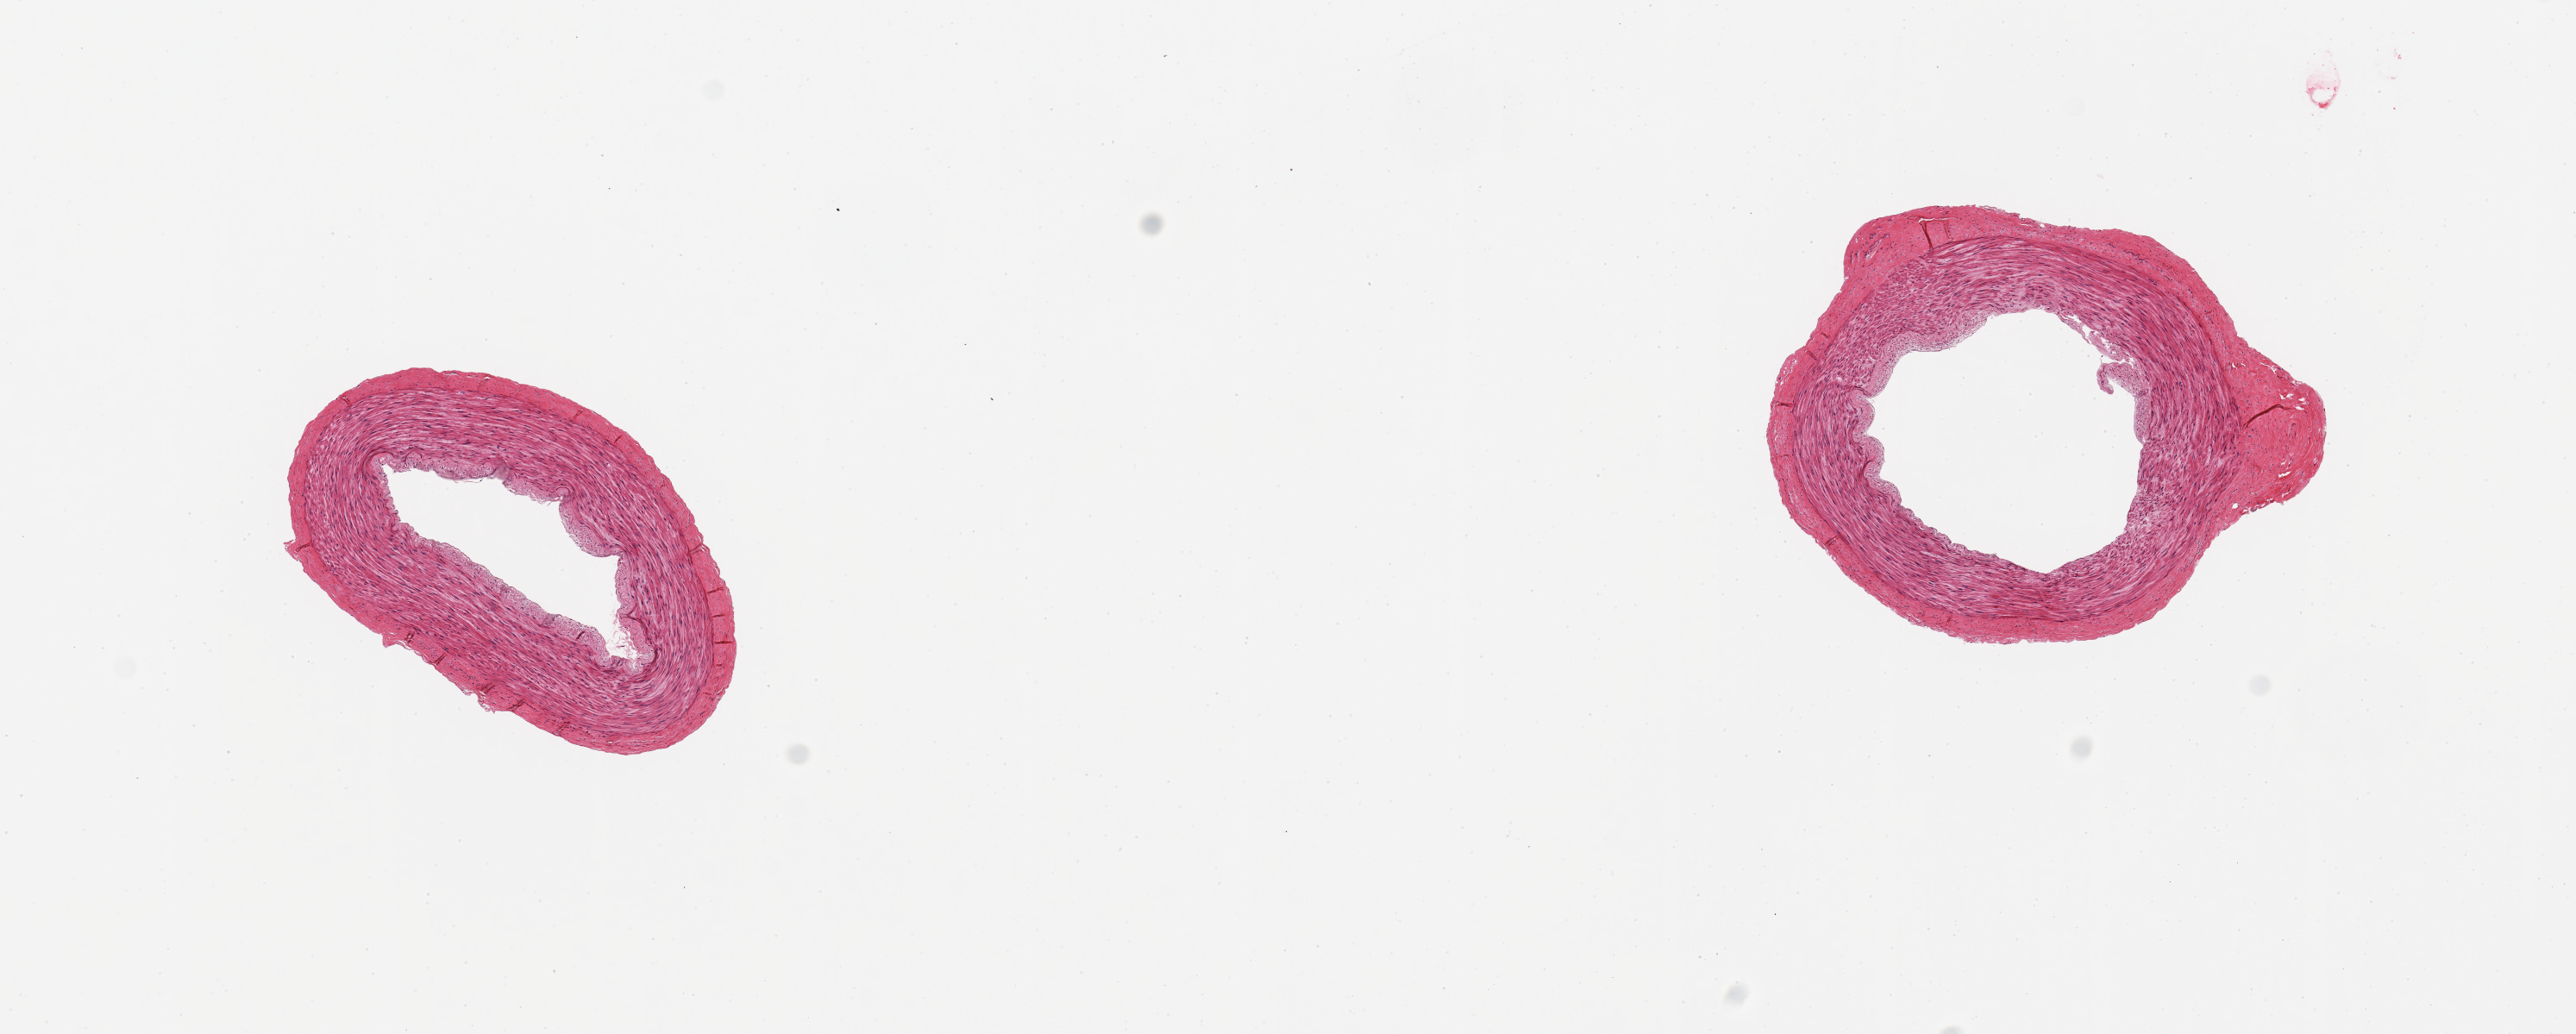
Digitized H&E-stained section, a low-resolution overview of the entire scanned area, about 11.8 x 4.7 mm. PAXgene-fixed paraffin-embedded (PFPE) section. Target tissue: tibial artery. Tissue donor sample. Donor: female.
* review note (as recorded): 2 pieces, no atherosis or adherent fat